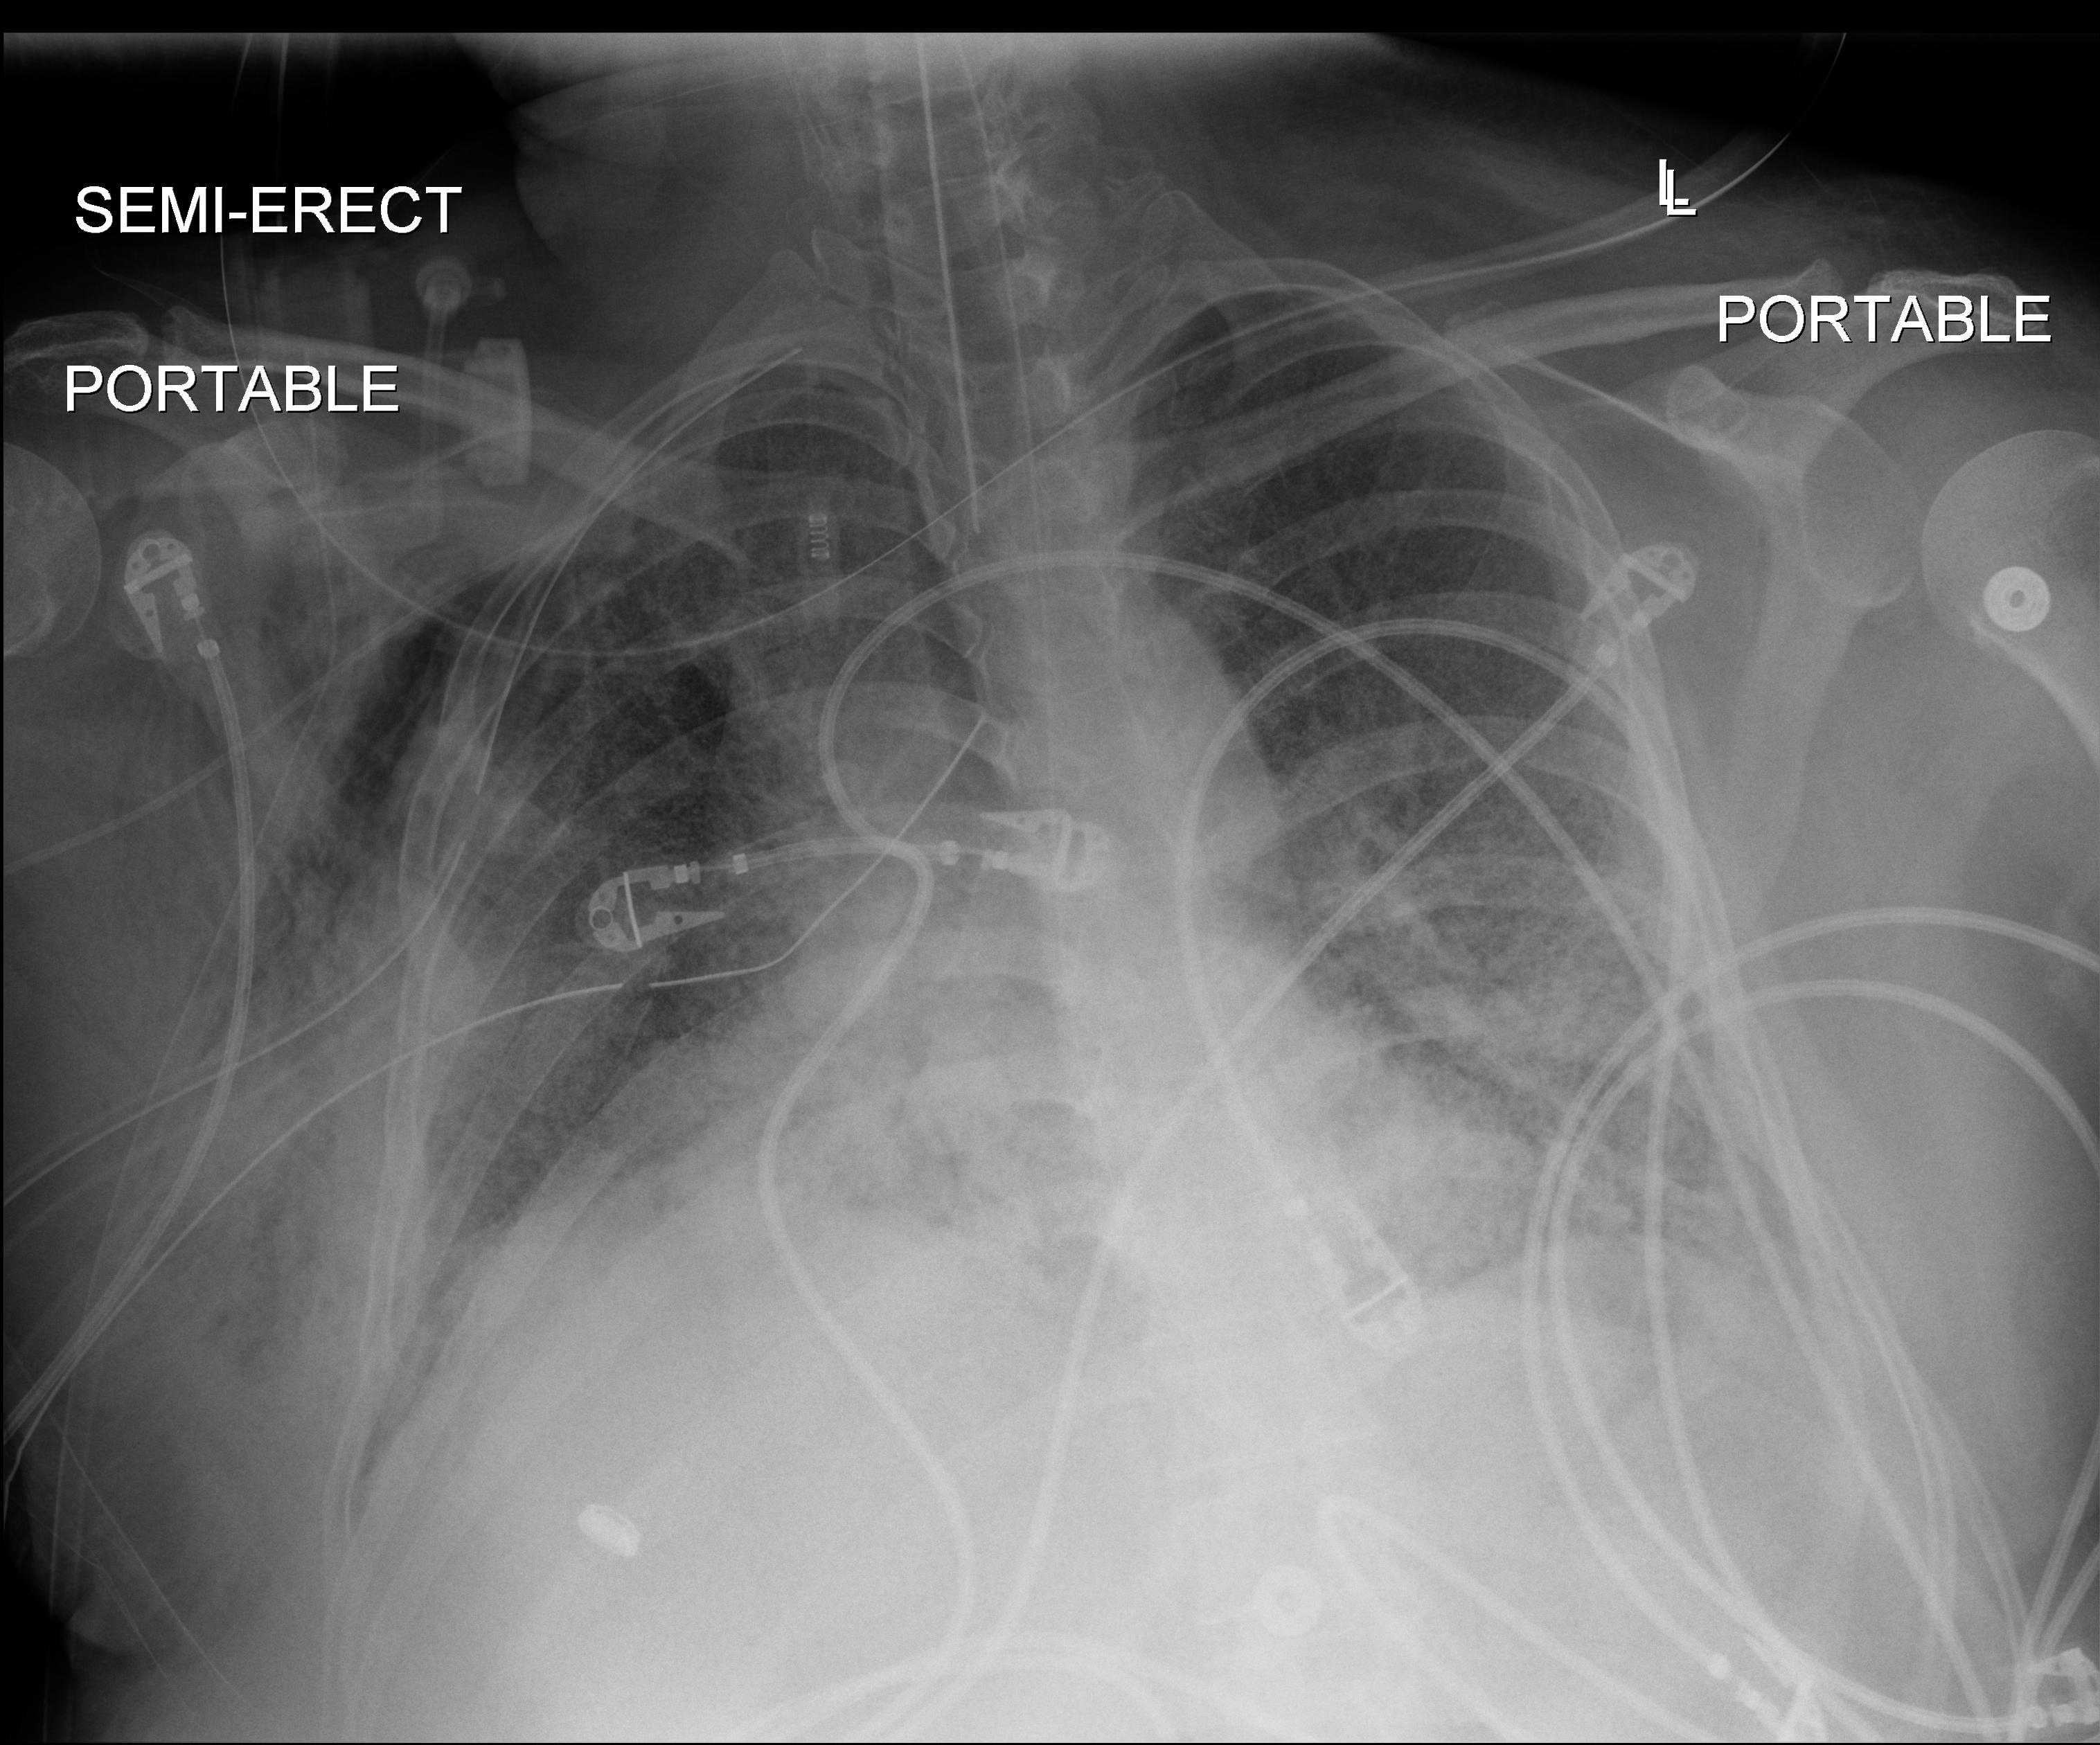
Chest X-ray (portable); anteroposterior (AP) projection. Patient hospitalised with COVID-19, aged 18–59 years.
Hospital-stay facts (about this admission, not read from this image; timing relative to this image not recorded): COPD (admission record): no.